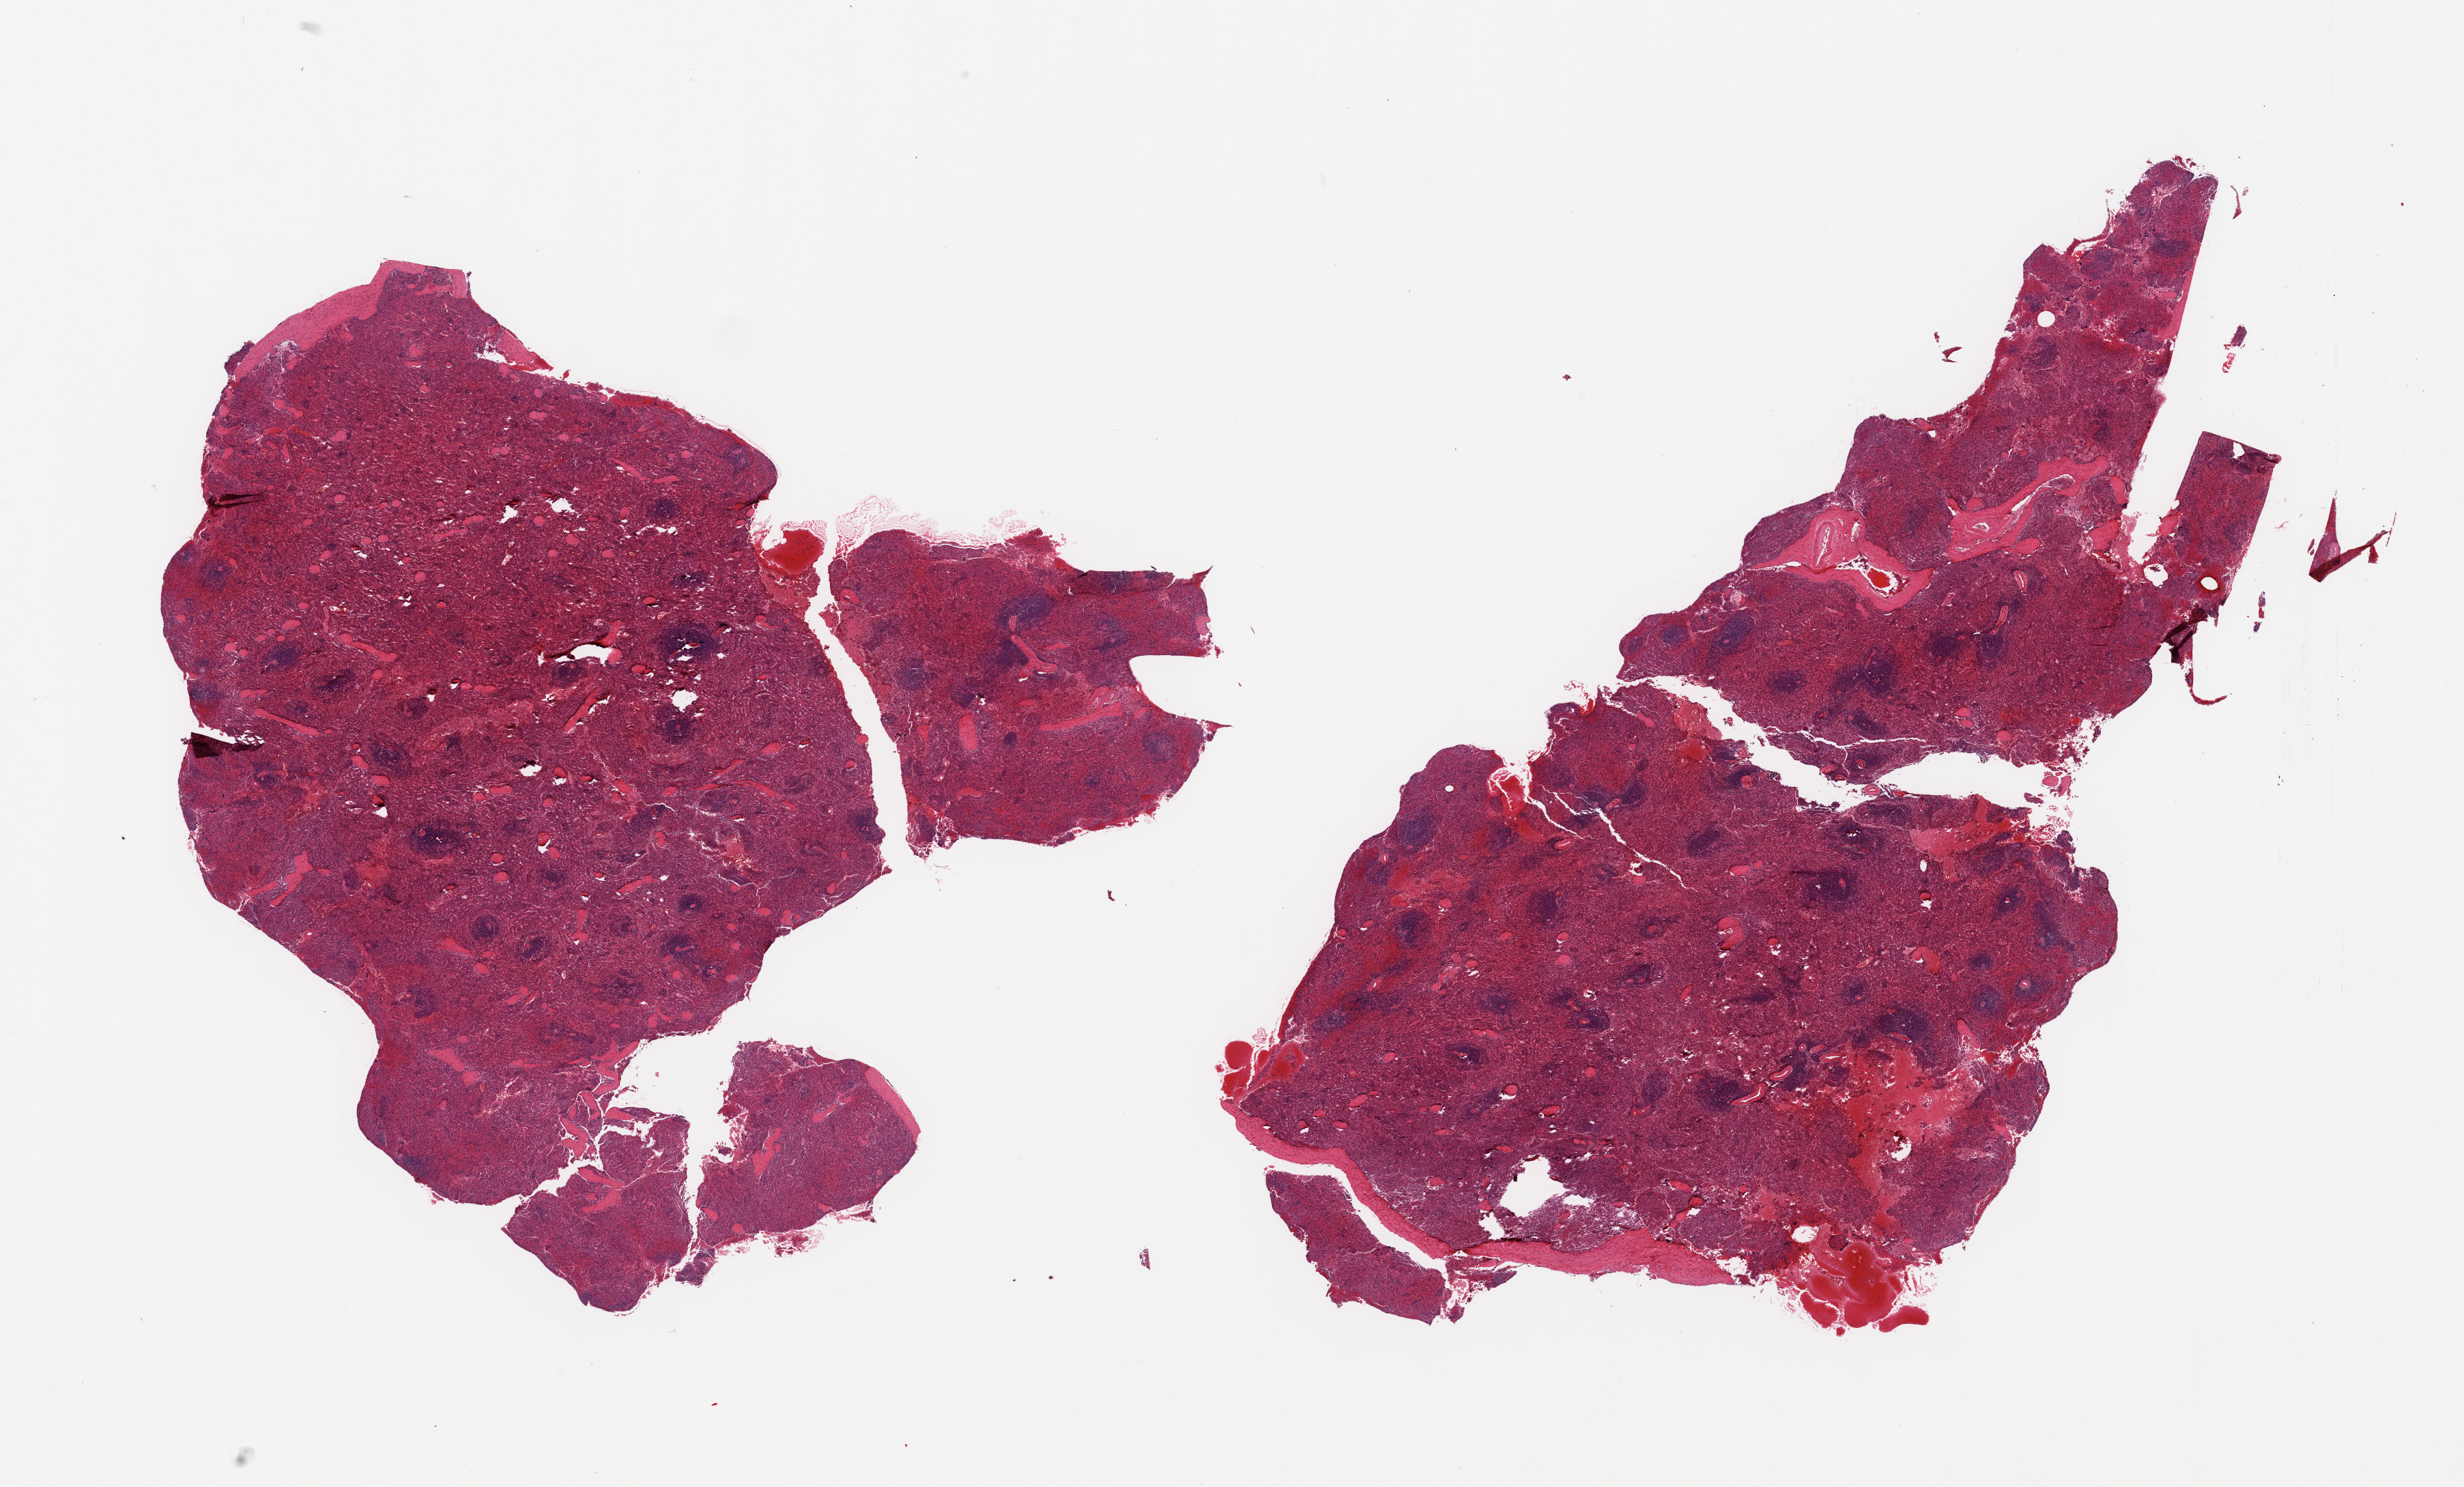
H&E whole-slide image, whole scanned area (about 28.5 x 17.2 mm) shown as a low-resolution overview; PAXgene-fixed, paraffin-embedded tissue; target tissue: spleen; donor tissue sample. Male donor.
Pathologist's review note for this sample: 2 fragmented pieces; moderate number of polymorphs in the red pulp.